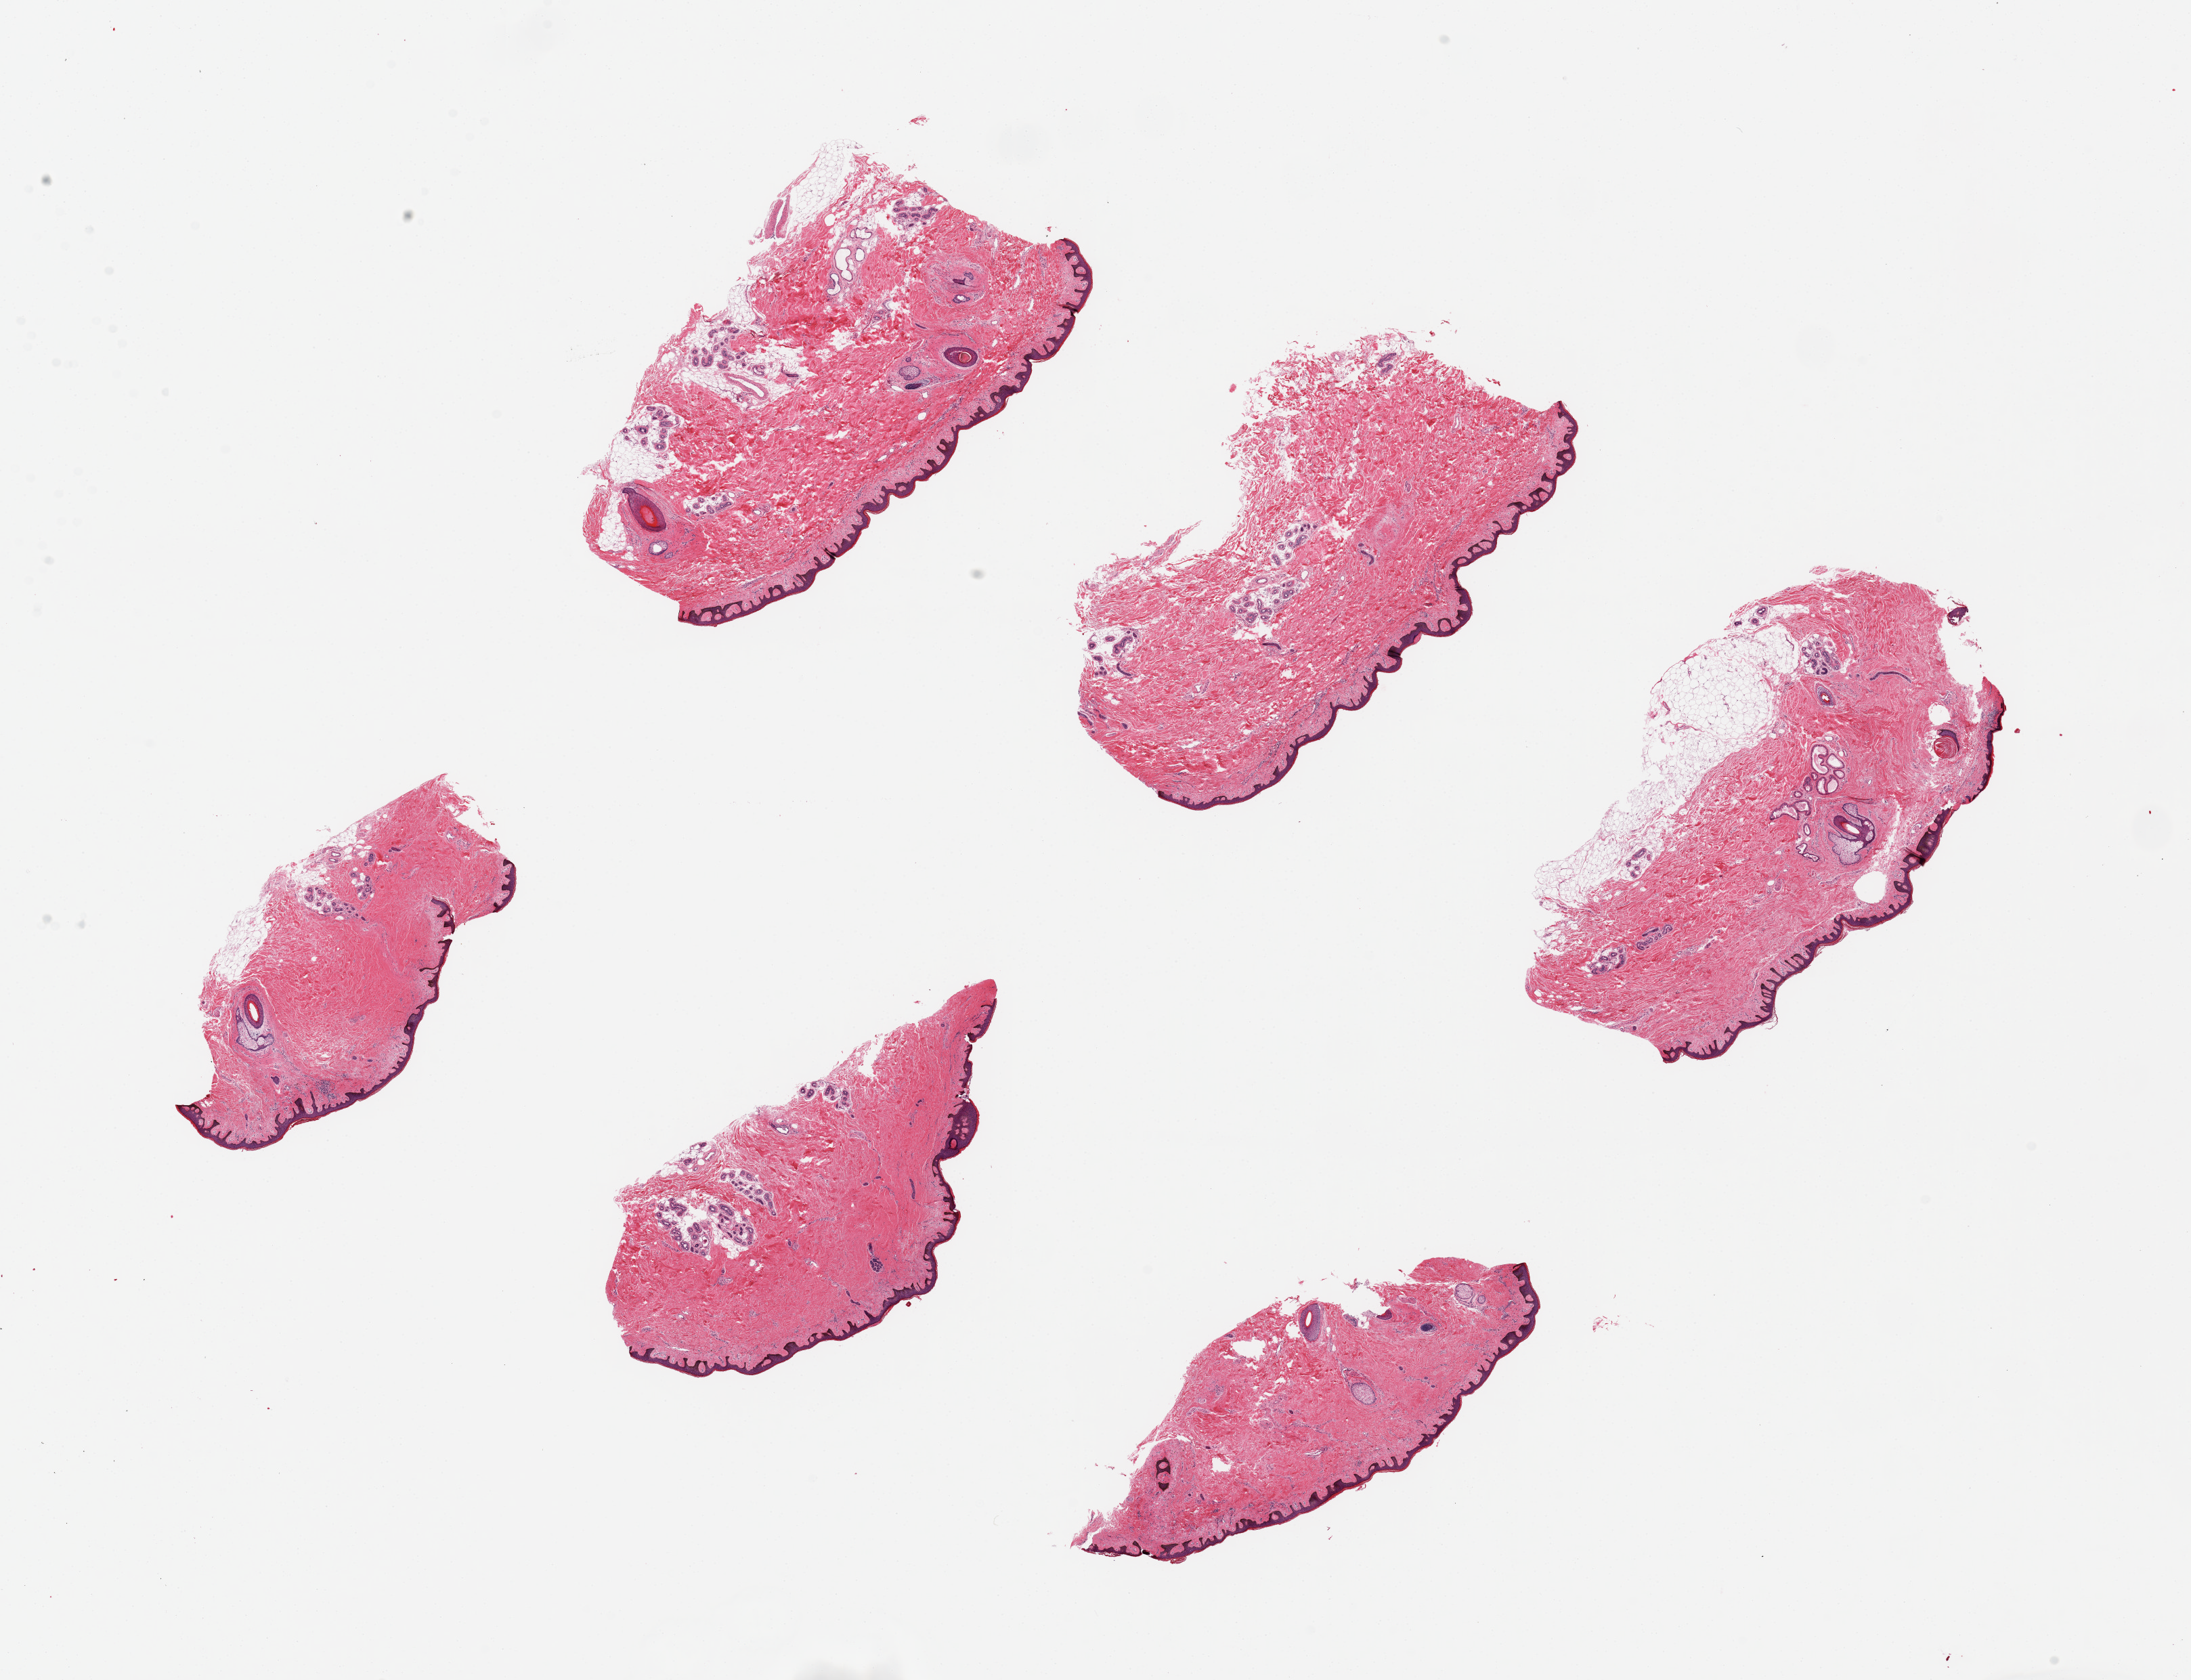
Digitized hematoxylin and eosin (H&E)-stained section, low-resolution overview of the scanned area, about 25.6 x 19.6 mm, PAXgene-fixed, paraffin-embedded tissue, sampled site (target tissue): skin of suprapubic region, tissue donor sample. Male donor.
- reviewer comment on this tissue sample: 6 pieces ~6x3mm, squamous epithelium is ~2% thickness